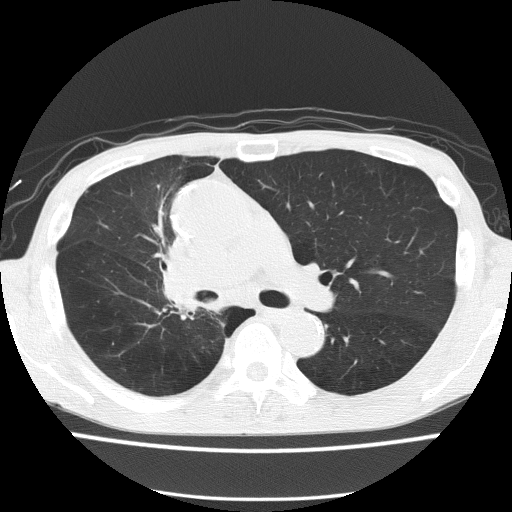
Low-dose screening chest CT, one axial slice; slice 92 of 150 in the series (ordered by position); reconstruction kernel FC51; 120 kVp; lung window (W 1500 / L -600 HU); 2 mm slice thickness; 512 × 512 image matrix, field of view 336 × 336 mm.
Outlined on this slice (expert manual segmentation):
- lesion 1 (tumor, hilum of right lung): bounding box <165,237,201,307> (left, top, right, bottom; pixels)